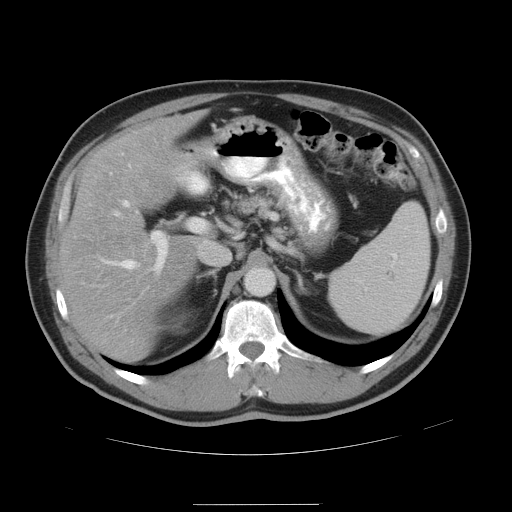
Contrast-enhanced abdominal CT, one axial slice. Slice 30 of 47 in the series (ordered by position). Soft-tissue window (W 400 / L 40 HU). 5 mm slice thickness. 512 × 512 image matrix, field of view 420 × 420 mm. Male patient, age 61 years. Case-level facts recorded for this patient, not image findings: diagnosis: colorectal cancer liver metastases, imaged before liver resection; multiple liver metastases: no; largest metastasis: 1.2 cm.
Structures marked on this image (outlined manually by an expert reader):
- hepatic veins: bounding box [x1, y1, x2, y2] px = [106, 164, 137, 268]
- liver: [64, 112, 200, 363]
- planned liver remnant (the part of the liver to remain after resection): [63, 113, 200, 363]
- portal vein (with intrahepatic branches): [115, 211, 206, 271]